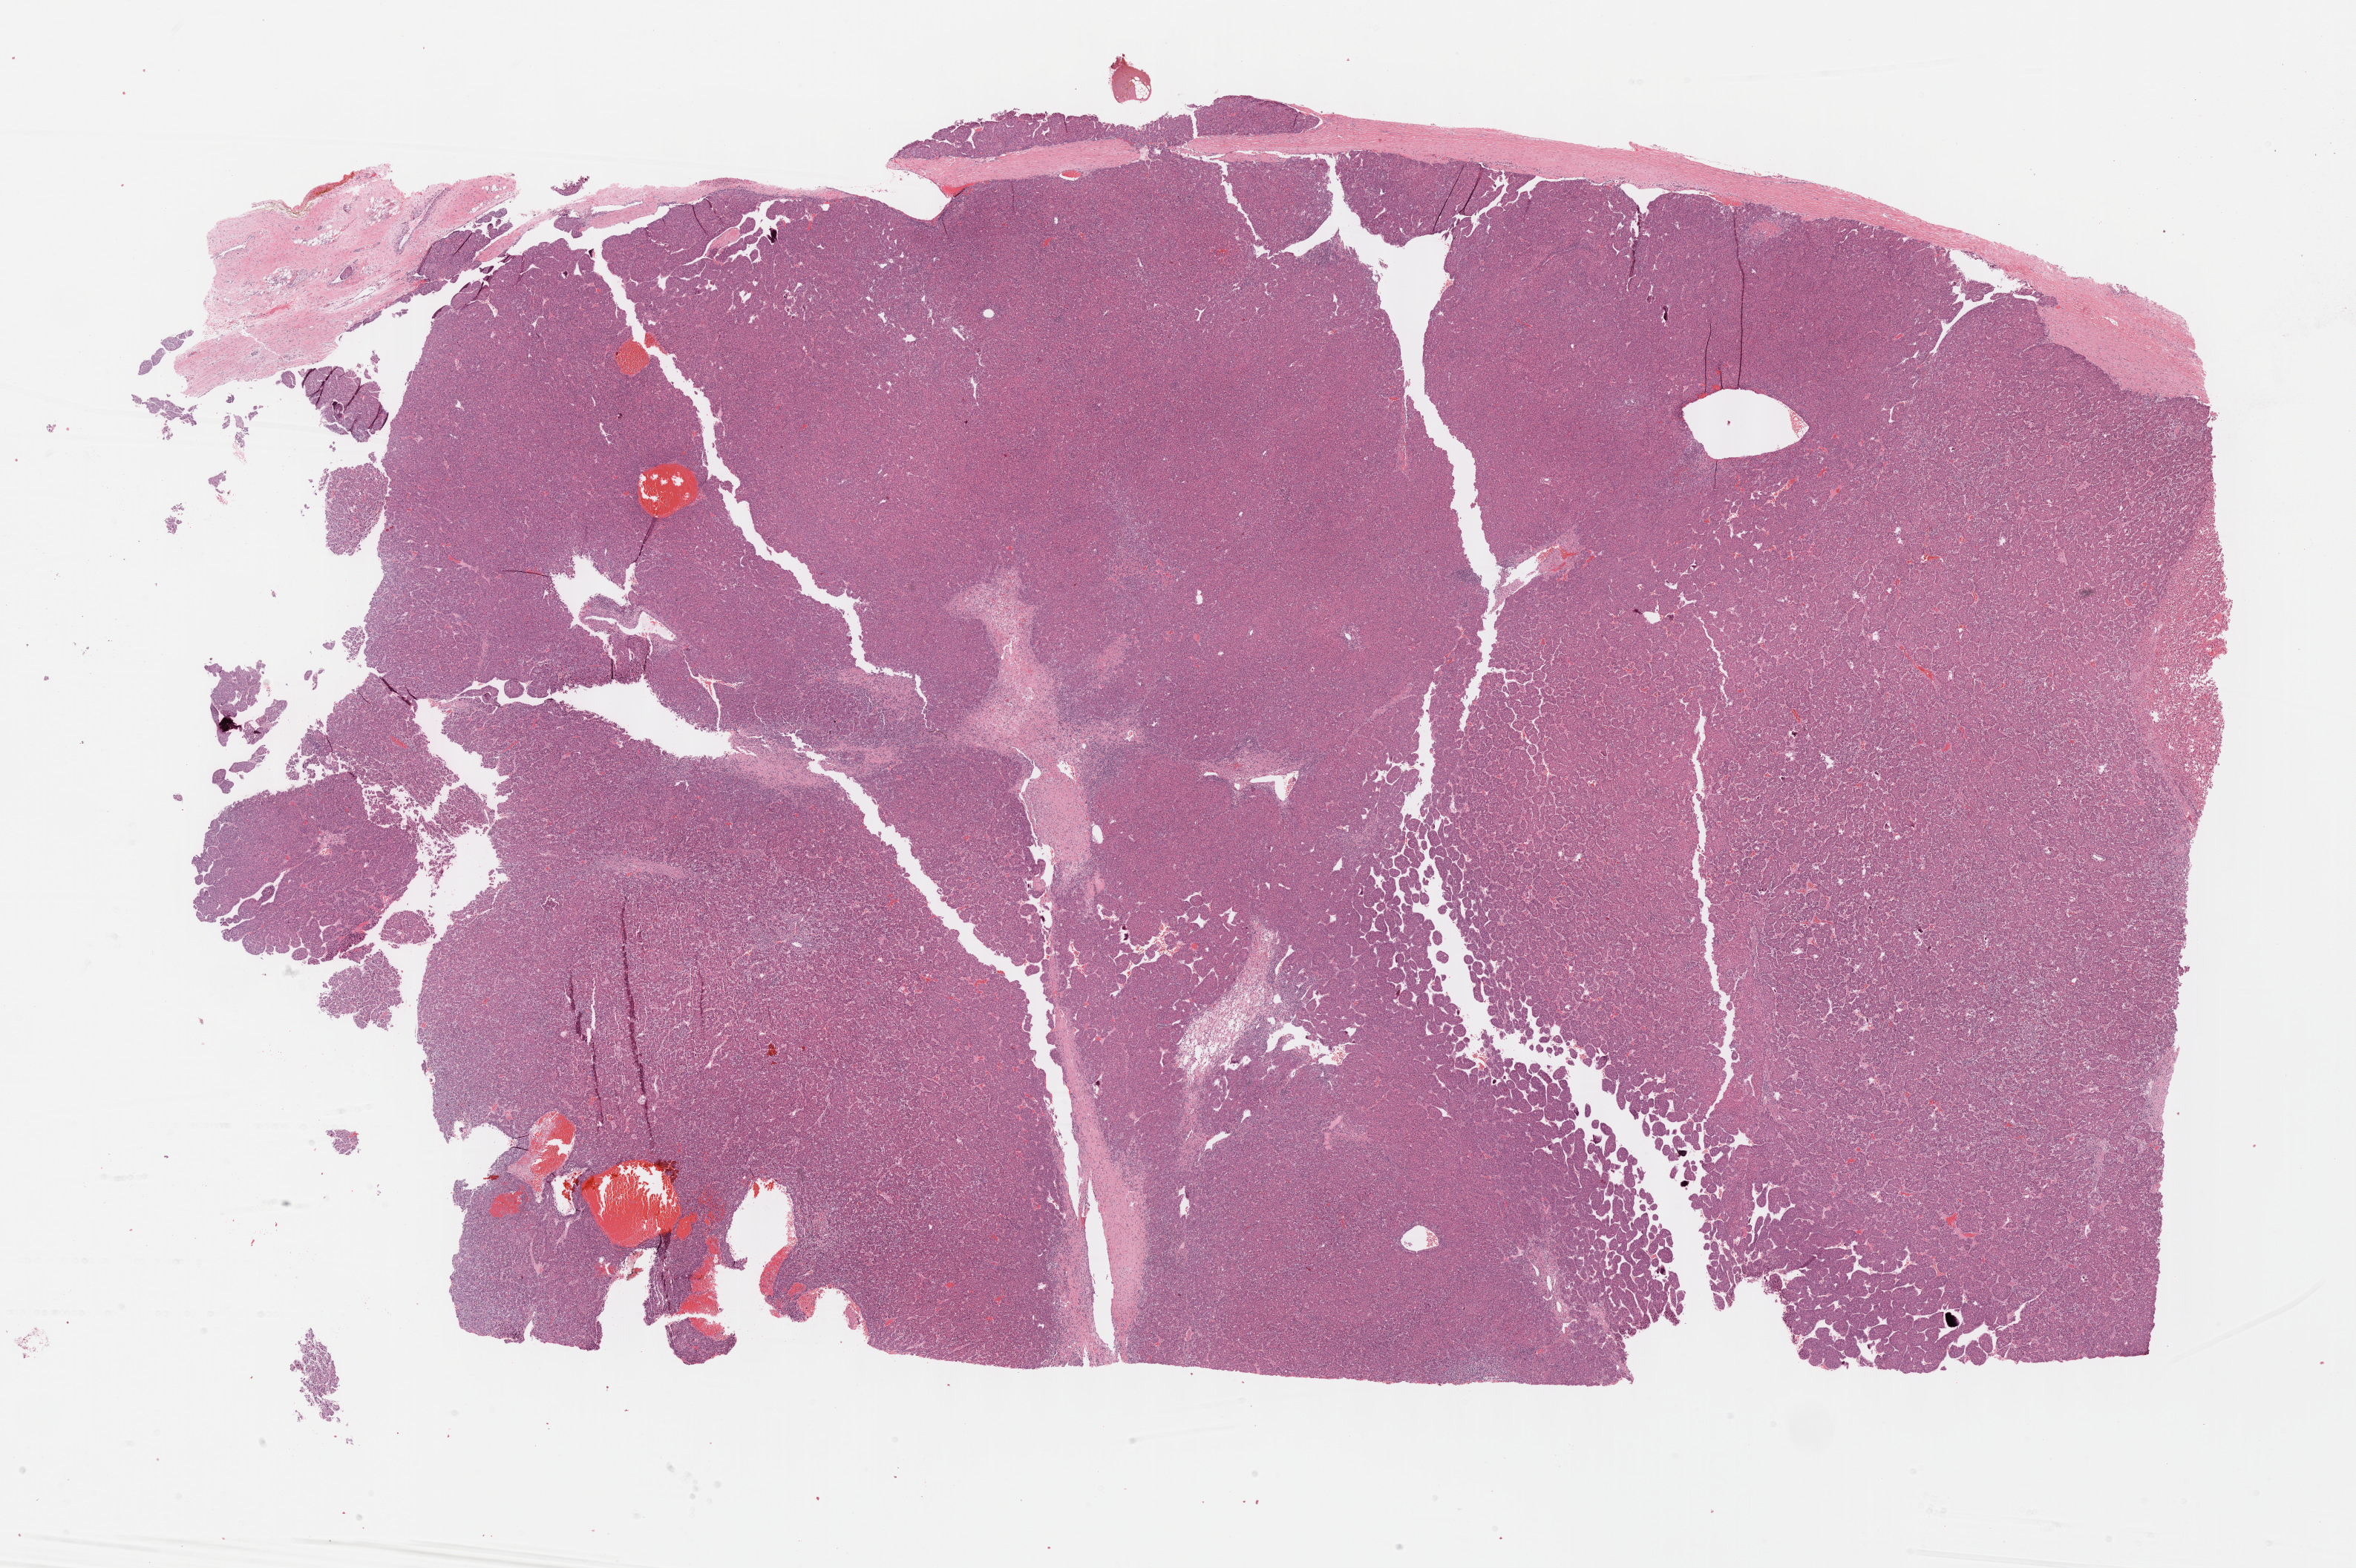
H&E whole-slide image, whole scanned area (about 25.7 x 17.1 mm, from a 40x scan) shown as a low-resolution overview. Formalin-fixed paraffin-embedded (FFPE) diagnostic section. Sample: primary tumour, liver. Patient: female, age at initial diagnosis 79 years.
Diagnosis: Hepatocellular carcinoma, NOS.